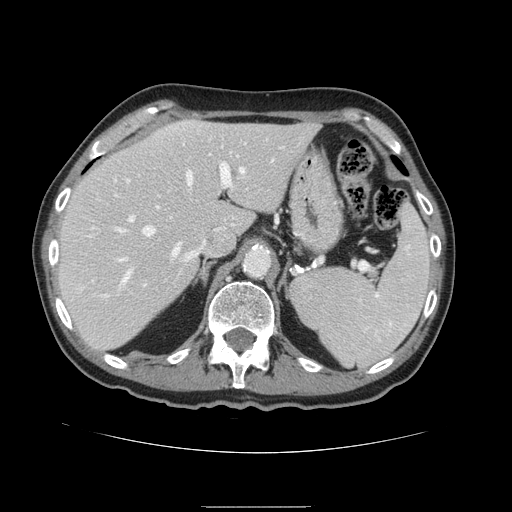
Contrast-enhanced abdominal CT, one axial slice; slice 106 of 168 in the series (ordered by position); 120 kVp; intravenous contrast given; soft-tissue window (W 400 / L 40 HU); 2.5 mm slice thickness; 512 × 512 image matrix, field of view 386 × 386 mm. Male patient, age 74 years. From the clinical record (not read from this slice): diagnosis: colorectal cancer liver metastases, imaged before liver resection; multiple liver metastases: no; largest metastasis: 14.5 cm; disease in both lobes: yes.
Structures marked on this image (expert manual segmentation):
- hepatic veins: bounding box <119,167,245,282> (left, top, right, bottom; pixels)
- liver: <58,120,320,351>
- planned liver remnant (the part of the liver to remain after resection): <58,120,320,350>
- portal vein (with intrahepatic branches): <95,163,232,254>